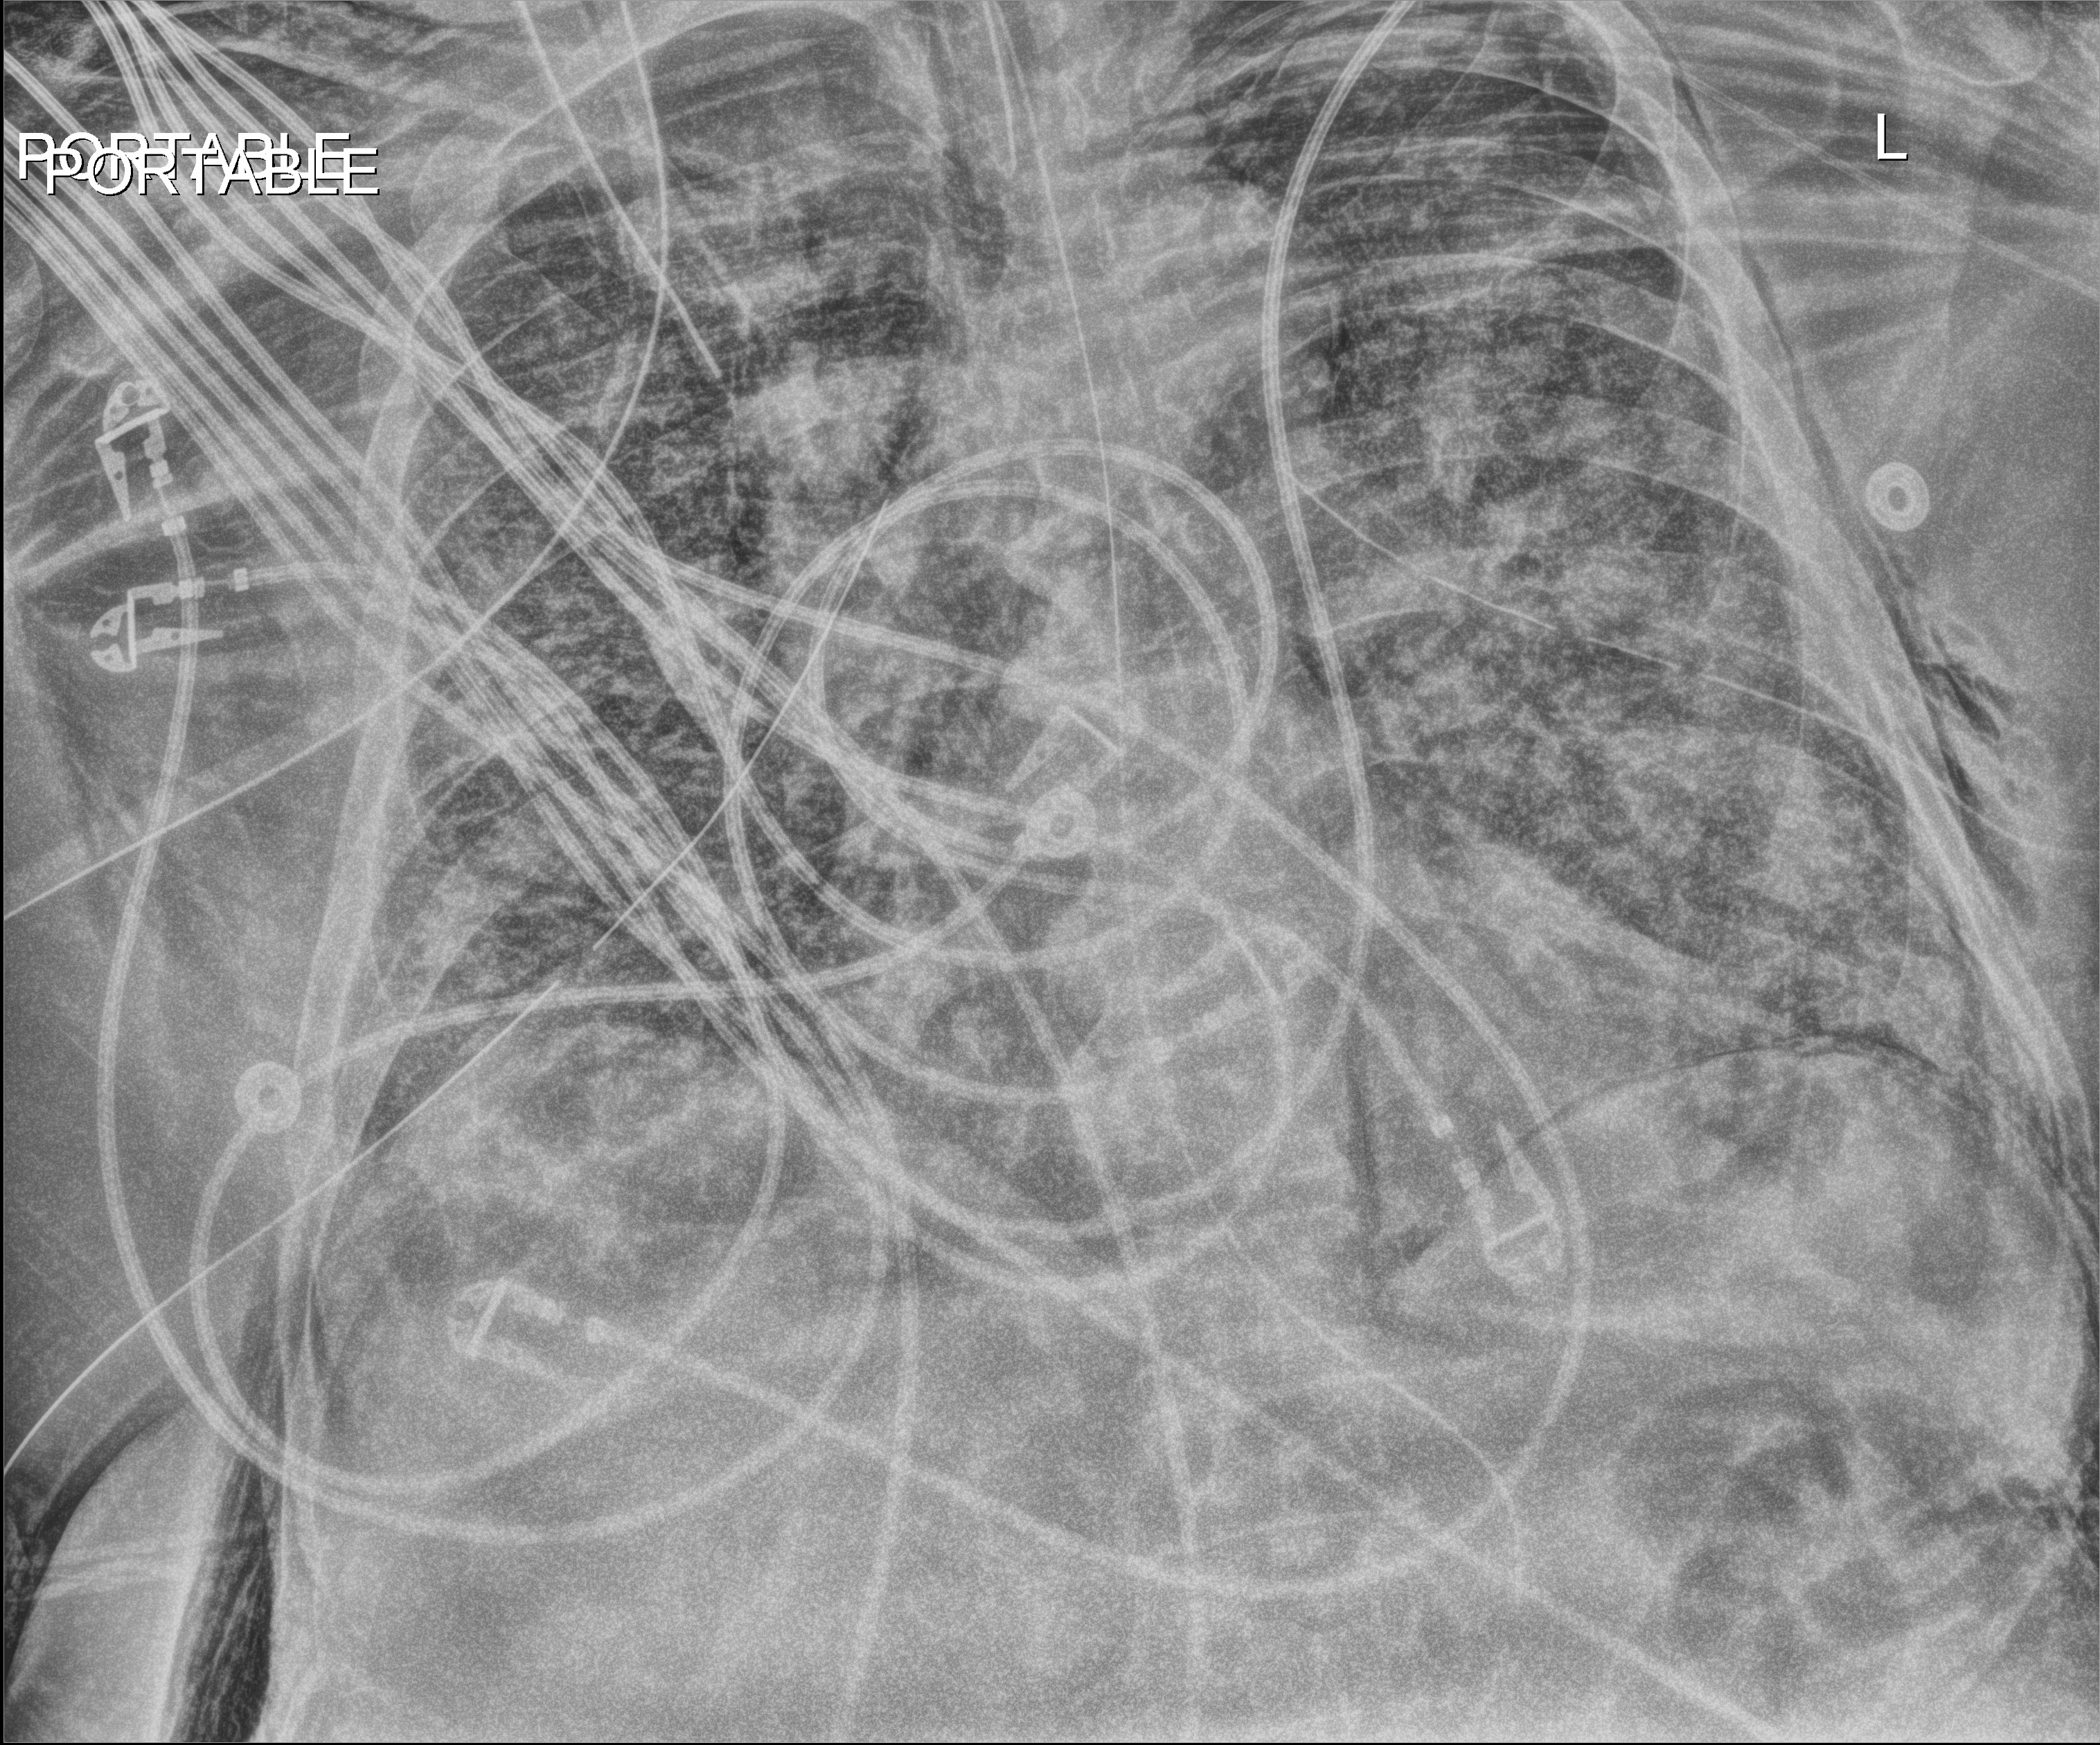
Chest radiograph. Adult patient hospitalised with COVID-19, age 18–59 years.
Hospital-stay facts (about this admission, not read from this image; timing relative to this image not recorded): chronic kidney disease (admission record): no.